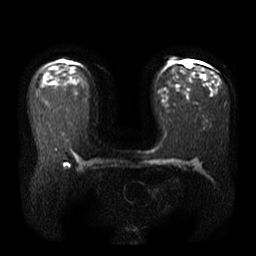
Breast MRI, one axial slice; slice 22 of 40 in the series (ordered by position); diffusion-weighted series; image 2 of 4 stored at this slice position (different b-values; order by instance number); 3 T; 5 mm slice thickness; 256 × 256 image matrix, field of view 380 × 380 mm. Female patient.
Annotated regions visible in this slice (outlined manually by an expert reader):
- tumour on diffusion-weighted imaging: bounding box <185,63,192,67> (left, top, right, bottom; pixels)